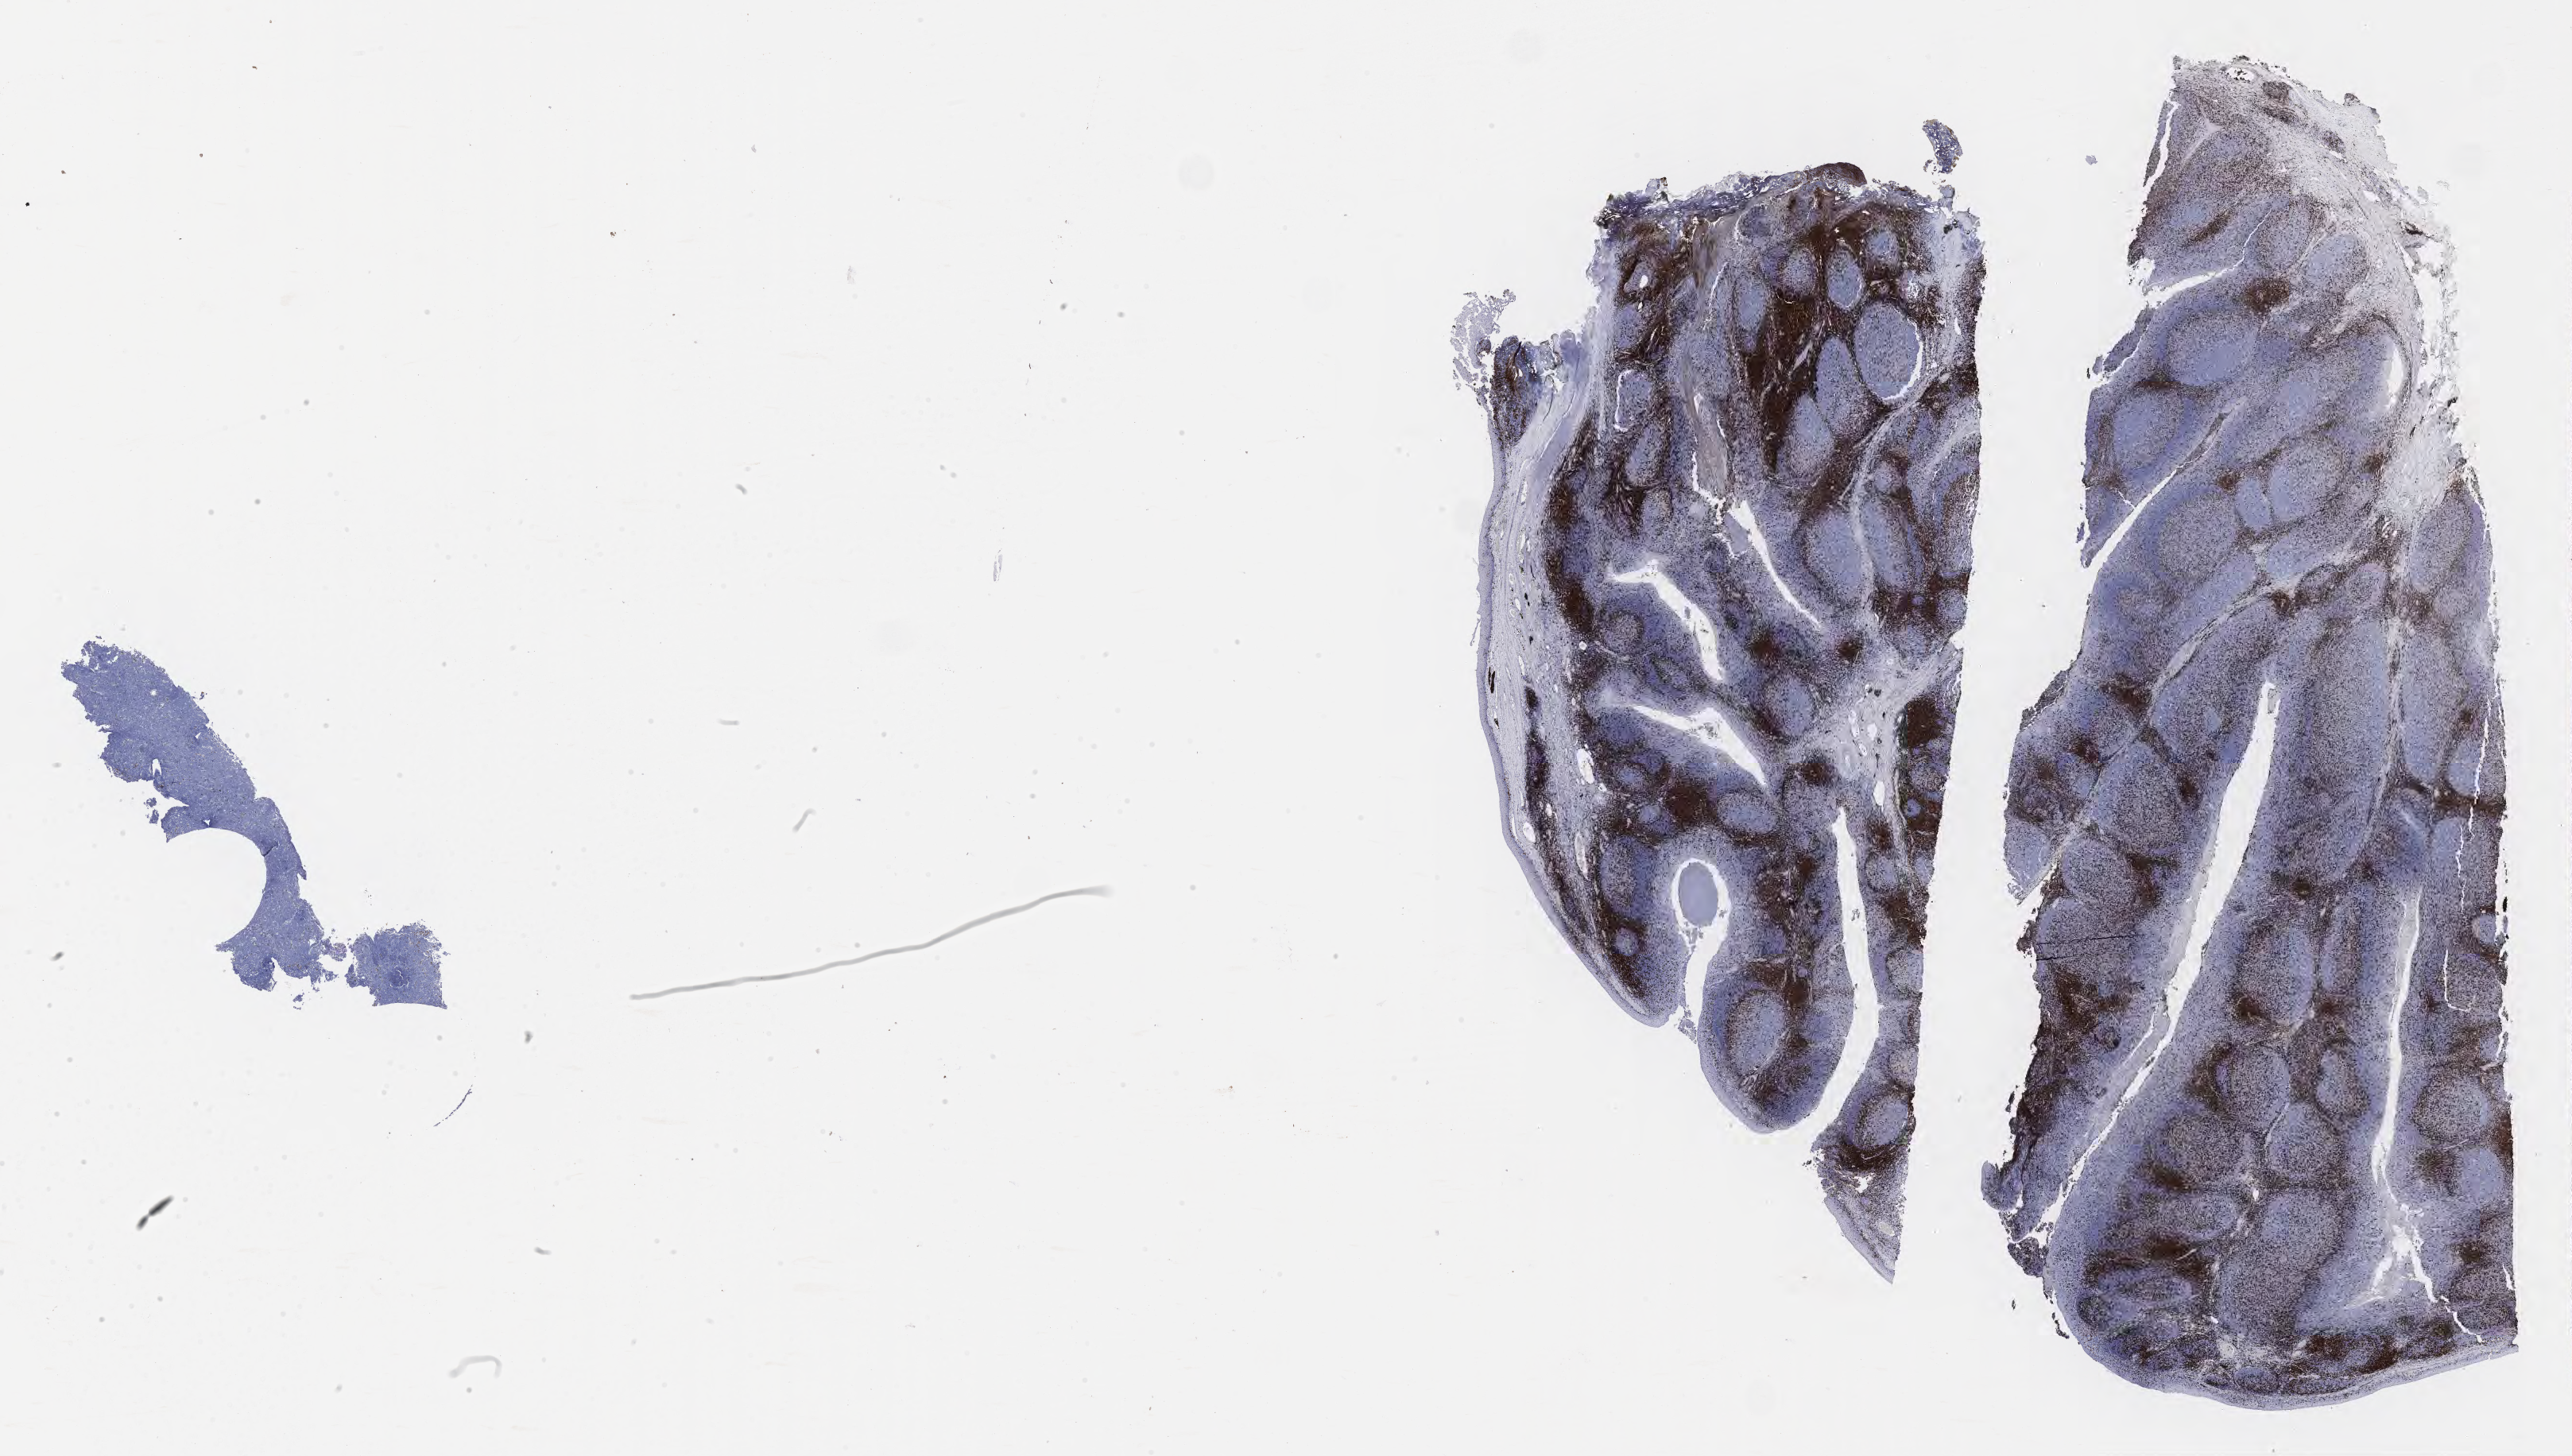
IHC for CD3, whole-slide image — shown as a low-resolution overview of the whole scanned area (about 26.2 x 14.8 mm). Tumor tissue. Patient: male, age at initial diagnosis 5 years.
- histologic diagnosis: Burkitt lymphoma, NOS